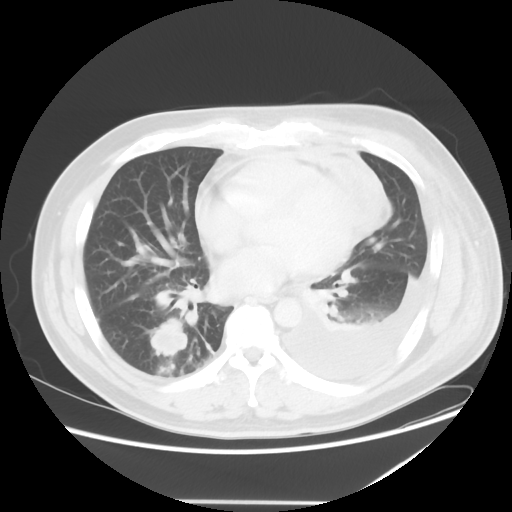
Chest CT, one axial slice. Position 21 of 52 along the scan axis. 120 kVp. Lung window (W 1500 / L -600 HU). 5 mm slice thickness. 512 × 512 image matrix, field of view 405 × 405 mm. Patient: male, 42 years. From the clinical record (not read from this slice): clinical TNM (as recorded): T2 N1 M1.
Annotated regions visible in this slice (rectangle marked by the reading radiologist):
- lung tumour (recorded histology: adenocarcinoma): bounding box <147,315,192,365> (left, top, right, bottom; pixels)